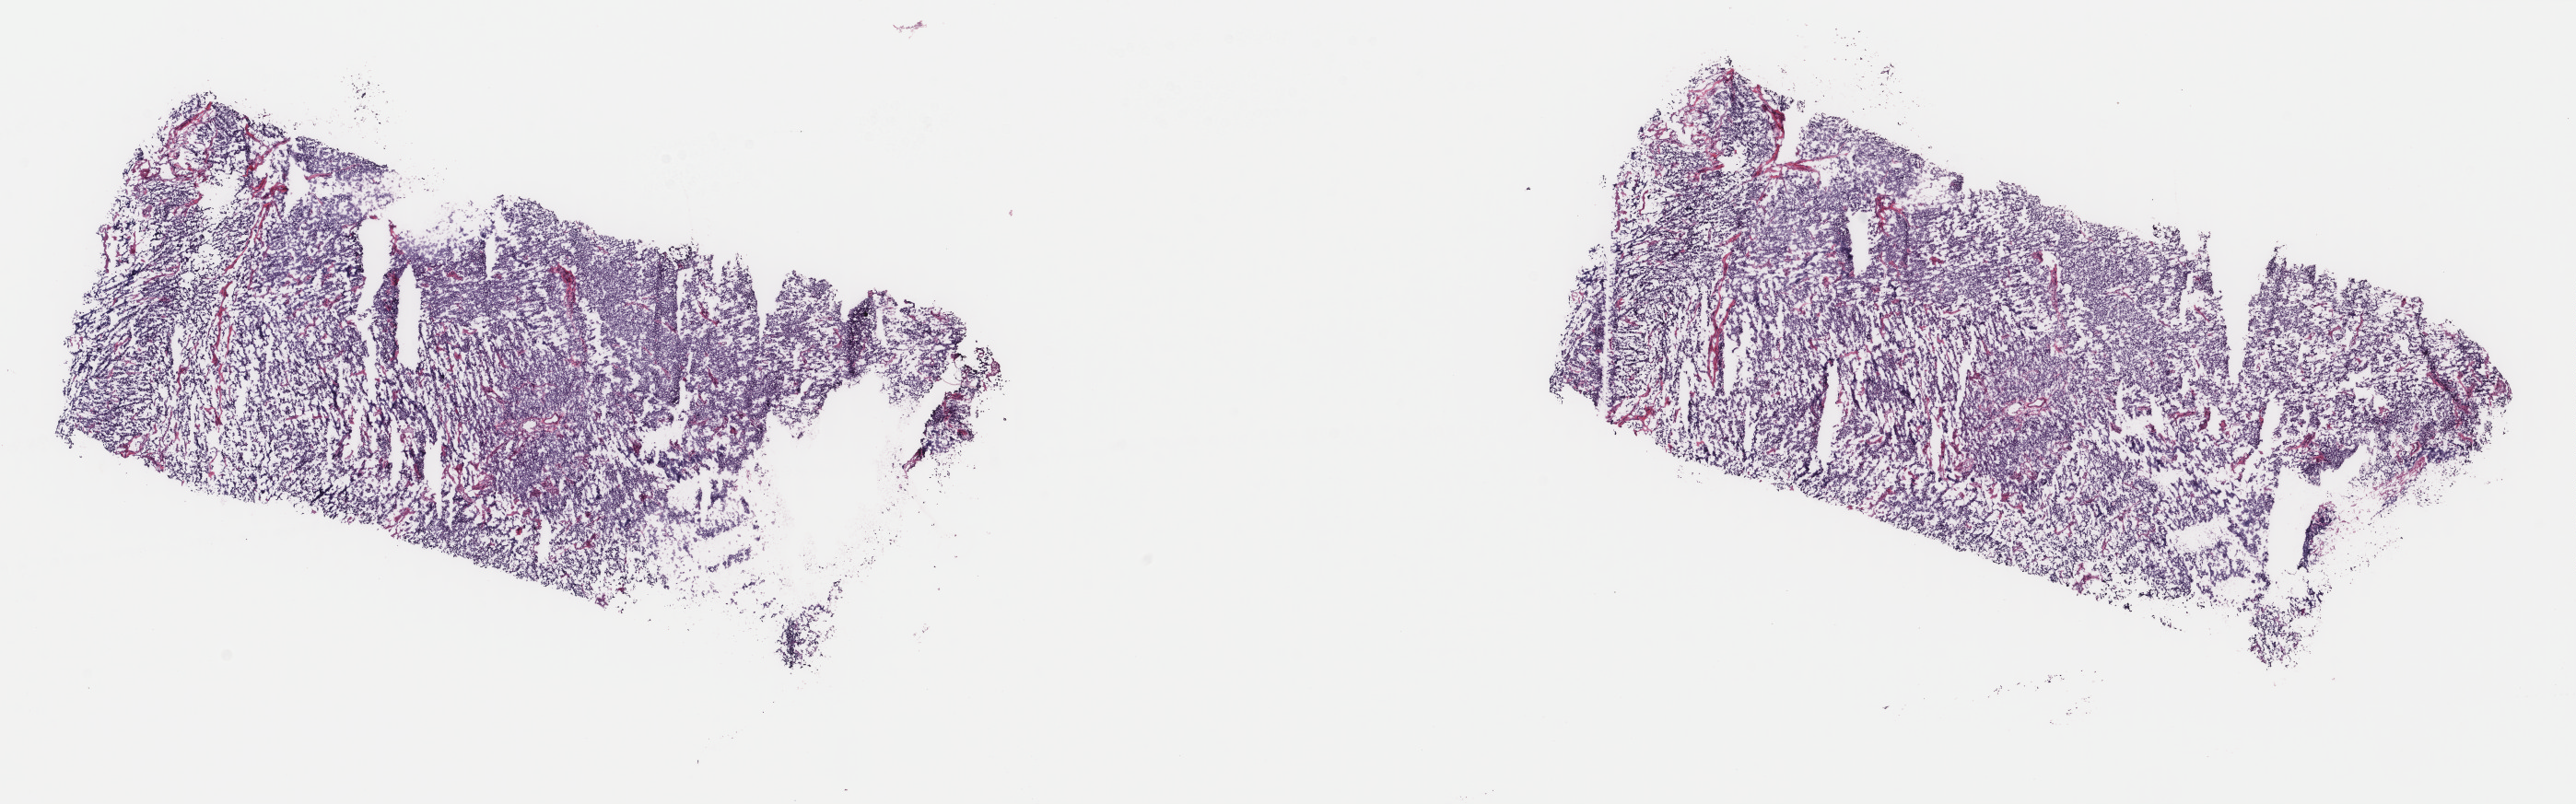
Whole-slide histology image, Hematoxylin and eosin (H&E) stained, shown as a low-resolution overview of the whole scanned area (about 22.2 x 6.9 mm, from a 40x scan). Frozen section. Sample: primary tumour, bladder. Male, age 54 years at initial diagnosis. Histologic grade: high grade. Pathologist review of this section (percent, as recorded): tumour cells 95%, tumour nuclei 90%, normal cells 0%, stromal cells 5%, necrosis 0%. Infiltration values recorded for this section: lymphocyte infiltration 0%, monocyte infiltration 0%, neutrophil infiltration 0%.
AJCC pathologic stage: III (7th edition). Pathologic diagnosis: Transitional cell carcinoma (dome of bladder).